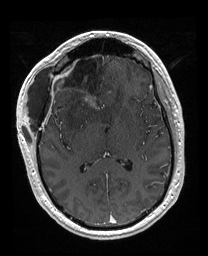
Brain MRI from a brain-tumour surgery series, one axial slice; position 92 of 176 along the scan axis; T1-weighted post-contrast; 1 mm slice thickness; 208 × 256 image matrix, field of view 208 × 256 mm. From the clinical record (not read from this slice): histopathology: Astrocytoma; WHO grade: 4; IDH mutation: yes; tumour location: Right Orbitofrontal Anterior Temporal Insular.
Structures marked on this image (outlined manually by an expert reader):
- previous resection cavity: bounding box (x1, y1, x2, y2) in pixels: (56, 52, 106, 111)